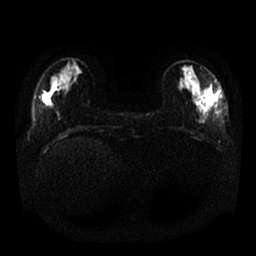
Breast MRI, one axial slice. Position 7 of 25 along the scan axis. Diffusion-weighted series; image 2 of 4 stored at this slice position (different b-values; order by instance number). 1.5 T. 4 mm slice thickness. 256 × 256 image matrix, field of view 340 × 340 mm. Female patient.
Structures marked on this image (outlined manually by an expert reader):
- tumour on diffusion-weighted imaging: bounding box [x1, y1, x2, y2] px = [207, 82, 216, 102]